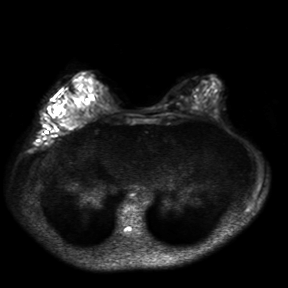
Breast MRI, one axial slice. Diffusion-weighted series; image 2 of 4 stored at this slice position (different b-values; order by instance number). 3 T. 4 mm slice thickness. 288 × 288 image matrix, field of view 360 × 360 mm. Female patient.
Outlined on this slice (outlined manually by an expert reader):
- tumour on diffusion-weighted imaging: bounding box <53,106,62,116> (left, top, right, bottom; pixels)